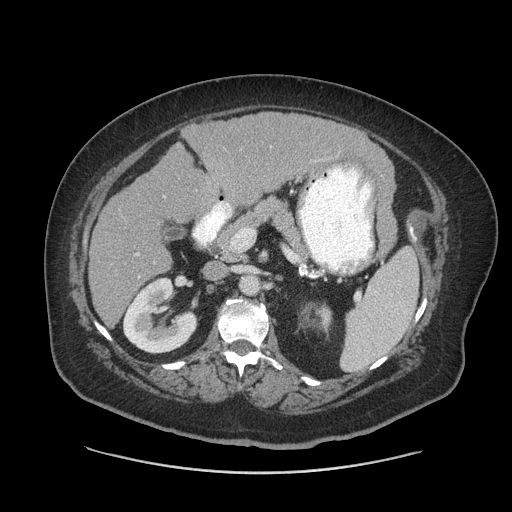
Contrast-enhanced abdominal CT (liver protocol), one axial slice. Slice 35 of 91 in the series (ordered by position). 140 kVp. Soft-tissue window (W 400 / L 40 HU). 2.5 mm slice thickness. 512 × 512 image matrix, field of view 420 × 420 mm. From the clinical record (not read from this slice): diagnosis: hepatocellular carcinoma (patient treated with transarterial chemoembolisation; whether this scan precedes or follows treatment is not stated here); TNM stage (as recorded): Stage-I; Child-Pugh class: A.
Annotated regions visible in this slice (semi-automatically segmented with operator editing):
- liver parenchyma outside the tumour (the mass and vessels are separate outlines, so this box may not span the whole liver): bounding box [x1, y1, x2, y2] px = [88, 112, 390, 326]
- liver vessels: [136, 253, 139, 256]